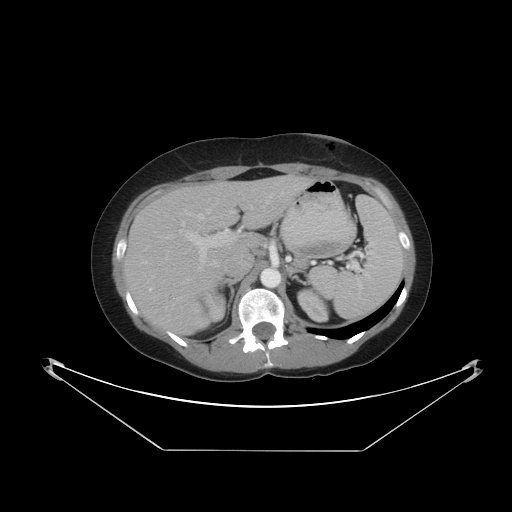
Contrast-enhanced abdominal CT, one axial slice; slice 29 of 48 in the series (ordered by position); reconstruction kernel STANDARD; 120 kVp; intravenous contrast given; soft-tissue window (W 400 / L 40 HU); 5 mm slice thickness; 512 × 512 image matrix. Female patient, age 38 years. Case-level facts recorded for this patient, not image findings: diagnosis: colorectal cancer liver metastases, imaged before liver resection; multiple liver metastases: yes; largest metastasis: 2.5 cm; disease in both lobes: no.
Outlined on this slice (outlined manually by an expert reader):
- hepatic veins: box from (x=166, y=192) to (x=241, y=258) px
- liver: (x=123, y=177)–(x=309, y=336)
- planned liver remnant (the part of the liver to remain after resection): (x=164, y=177)–(x=306, y=252)
- portal vein (with intrahepatic branches): (x=179, y=195)–(x=272, y=270)